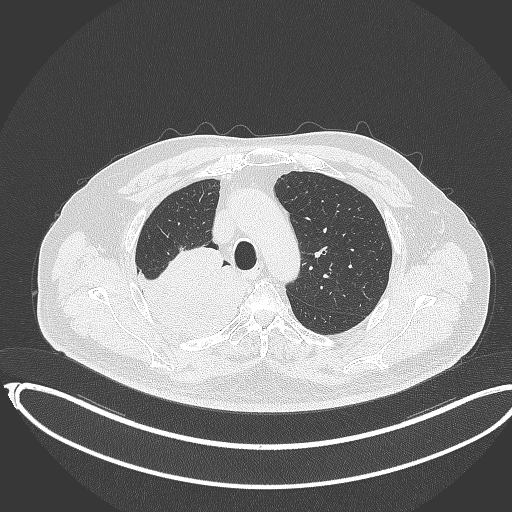
Chest CT, one axial slice; position 274 of 403 along the scan axis; reconstruction kernel B70f; 120 kVp; lung window (W 1500 / L -600 HU); 1 mm slice thickness; 512 × 512 image matrix. Male patient, age 68 years. From the clinical record (not read from this slice): clinical TNM (as recorded): T2a N0 M0.
Structures marked on this image (rectangle marked by the reading radiologist):
- lung tumour (recorded histology: adenocarcinoma): bounding box [x1, y1, x2, y2] px = [130, 242, 252, 348]